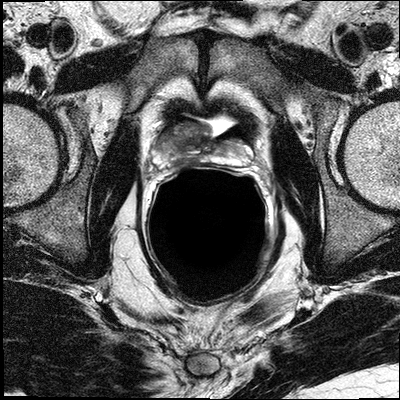
Multiparametric prostate MRI examination; 3 images, each a single mid-volume slice chosen by position (not for content). Treatment context recorded for this patient: No surgery, ADT with RT.
Image 1: T2-weighted axial slice, series "T2W_TSE_AX", slice 17 of 32.
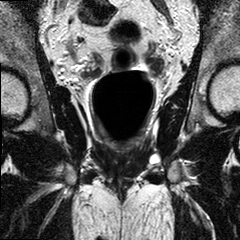
Image 2: T2-weighted coronal slice, slice 13 of 24, 3 mm slice thickness.
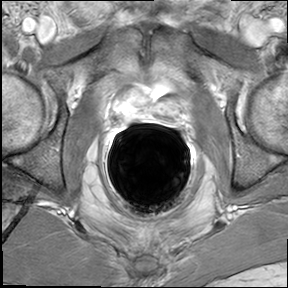
Image 3: DCE (dynamic gadolinium-enhanced) axial slice, series "AX BLISS_GAD_8", slice 17 of 32, dynamic phase 5 of 8.
MRI report (verbatim):
FINDINGS: Status post TURP. There is a diffuse T2-weighted hypointense signal alterations seen the right peripheral zone and a smaller portion of the right central gland, predominantly in the midthird and base, with suspicious rapid wash in and wash out on the dynamic series. This is suspicious for malignancy. There is no extracapsular disease seen into the periprostatic tissues. The seminal vesicles show bilateral T2-hypointense signal, which abnormal enhancement on the dynamic series. This is suspicious for seminal vesicles infiltration. No evidence for involvement of the neurovascular bundle on either side. No evidence of involvement of bladder neck and rectal wall. No suspiciously enlarged obturator and iliac lymph nodes. Multiplanar reconstructions, subtraction images, and CAD analysis of the dynamic series for assessment of the kinetic information facilitated the interpretation of the exam. IMPRESSION: 1) Imaging findings suggestive for predominantly right-sided tumor without evidence of extraglandular extension into periprostatic tissues. No involvement of the neurovascular bundles on either side. However, there is abnormal enhancement and abnormal T2-weighted hypointense signal in the seminal vesicles, which is suggestive for seminal vesicles infiltration. No suspiciously enlarged obturator and iliac lymph nodes. 2) Status post TURP; 3) BPH

Biopsy pathology report for this patient (as recorded):
The specimen consists of multiple core fragments of tan soft tissue measuring from 0.3cm to 1.8cm in length and 0.1cm in diameter. The specimen is submitted in six cassettes.1-right pz, 2-right pz/tz, 3-right apex, 4-left pz, 5-left pz/tz, 6-left apex. PROSTATE 1. RIGHT PZ: PROSTATIC ADENOCARCINOMA, GLEASON GRADE 4+3=7/10, INVOLVING TWO CORES, ABOUT 30% OF TISSUE EXAMINED. 2. RIGHT PZ/TZ: PROSTATIC ADENOCARCINOMA, GLEASON GRADE 4+3=7/10, INVOLVING TWO CORES, ABOUT 10% OF TISSUE EXAMINED (SEE NOTE). 3. RIGHT APEX: PROSTATIC ADENOCARCINOMA, GLEASON GRADE 4+3=7/10, INVOLVING TWO CORES, ABOUT 20% OF TISSUE EXAMINED. 4. LEFT PZ: PROSTATIC ADENOCARCINOMA, GLEASON GRADE 3+3=6/10, INVOLVING ONE CORE, ABOUT 5% OF TISSUE EXAMINED (SEE NOTE). 5. LEFT PZ/TZ: BENIGN PROSTATIC TISSUE, NO TUMOR IDENTIFIED. 6. LEFT APEX: PROSTATIC TISSUE WITH MICROSCOPIC FOCUS OF ATYPICAL SMALL ACINAR PROLIFERATION